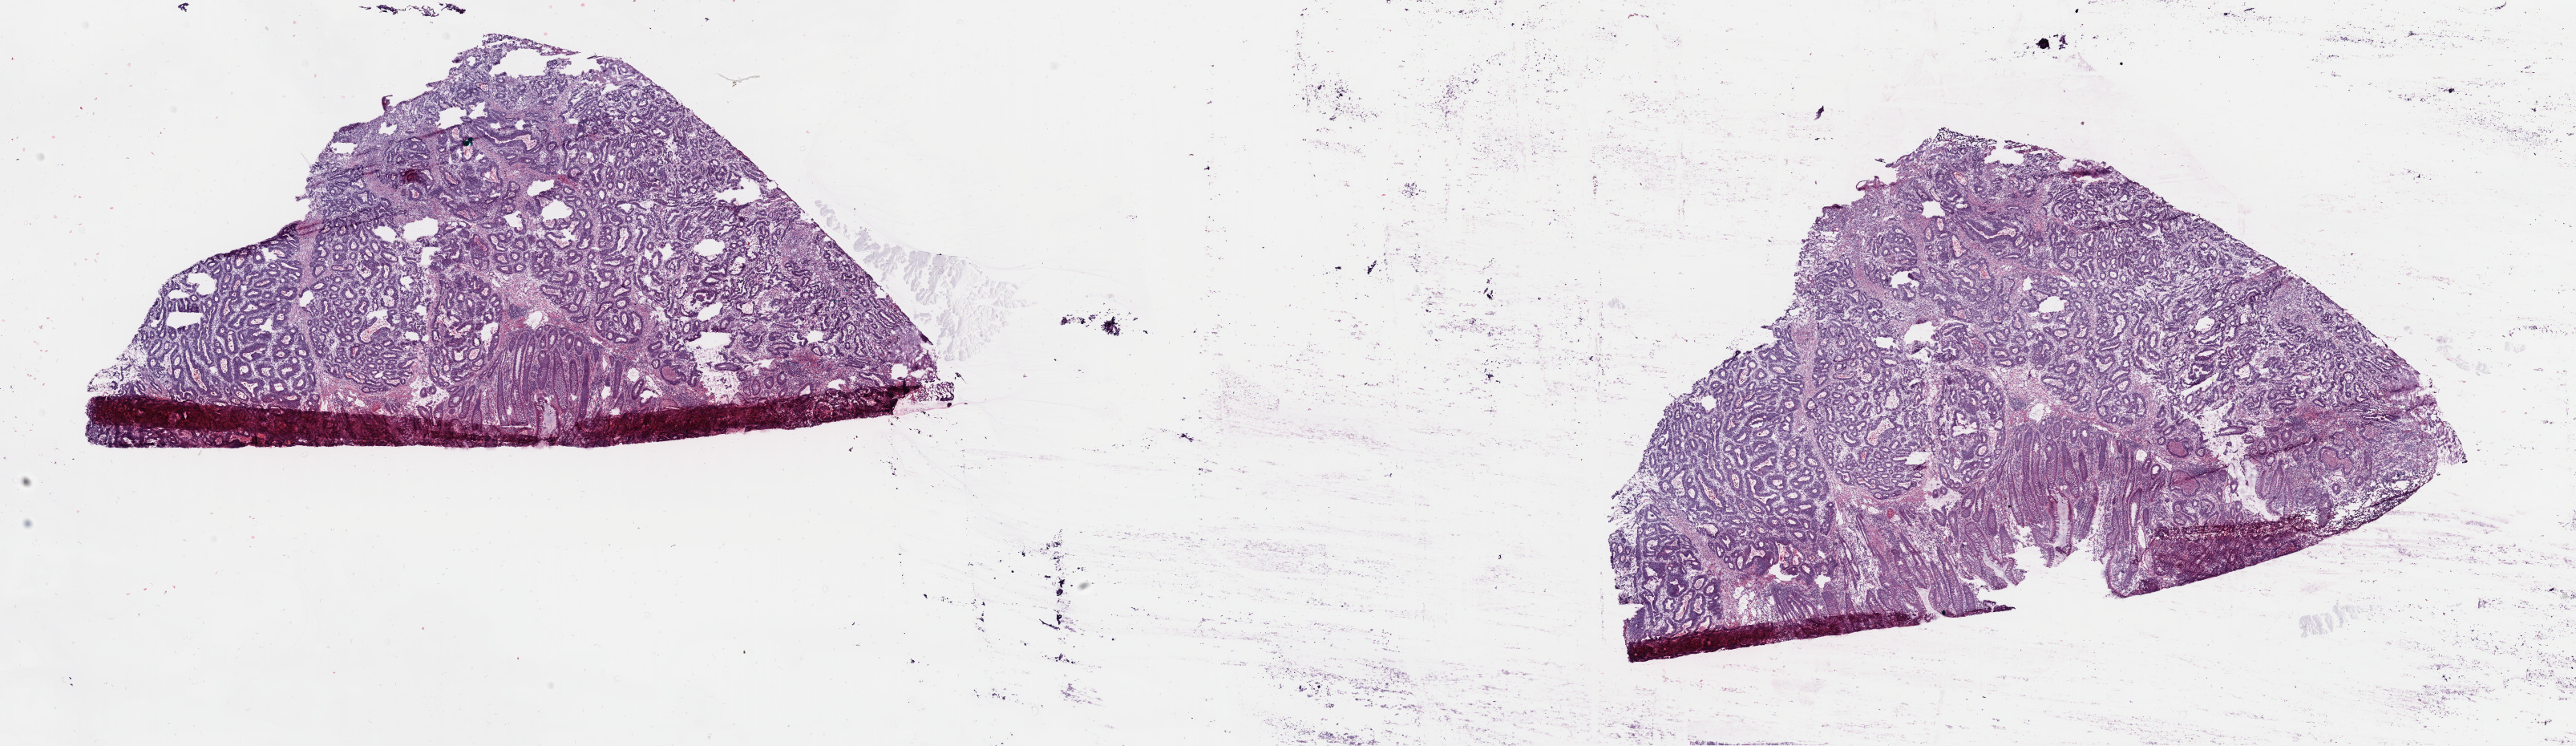
Digitized H&E tissue section (whole slide), whole scanned area (about 25.4 x 7.3 mm) shown as a low-resolution overview; frozen section; sample: primary tumour, colon. Male patient; age at initial diagnosis 76 years. Slide review estimates, as recorded: tumour cells 75%, tumour nuclei 60%, normal cells 15%, stromal cells 9%, necrosis 1%. Infiltration values recorded for this section: lymphocyte infiltration 12%, monocyte infiltration 3%, neutrophil infiltration 8%.
Lymph nodes positive (case pathology): 0 of 32 examined. Histologic diagnosis: Adenocarcinoma, NOS (sigmoid colon). AJCC pathologic stage: IIA (6th edition).